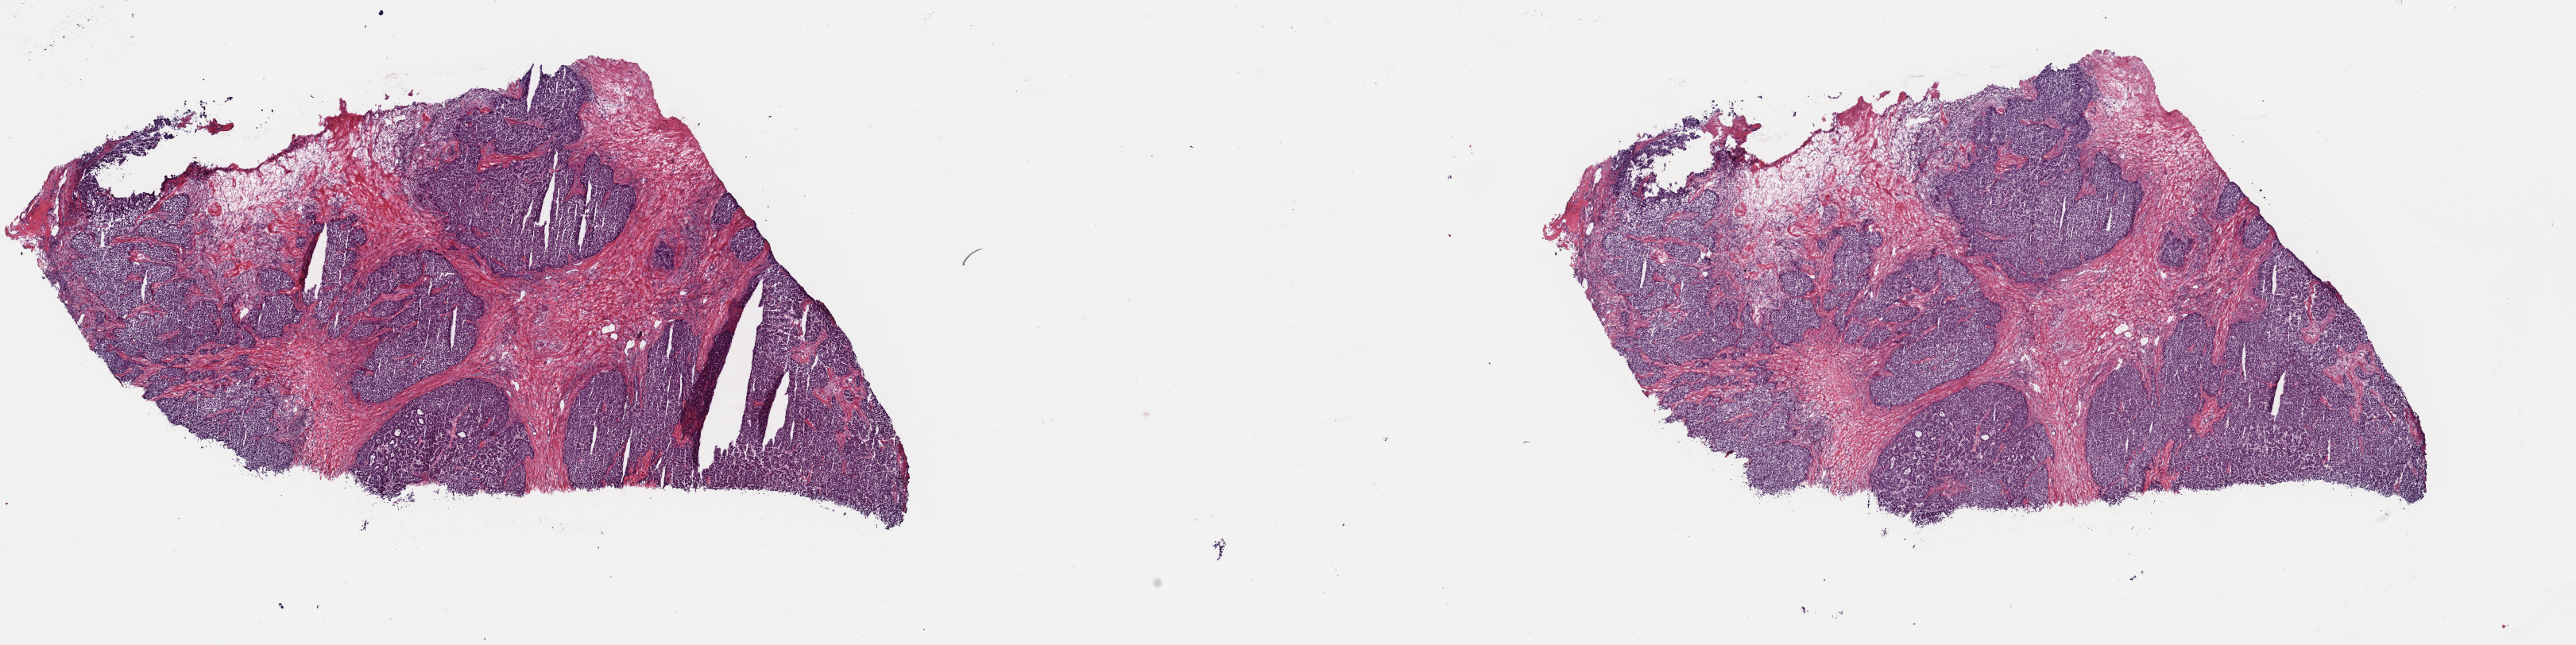
Whole-slide histology image, H&E, shown as a low-resolution overview of the whole scanned area (about 25.6 x 6.4 mm, acquisition: 40x scan), frozen section, liver, primary tumour sample. Patient: female, age at initial diagnosis 54 years. Histologic grade: G2 (moderately differentiated). Slide review estimates, as recorded: tumour cells 50%, tumour nuclei 100%, normal cells 0%, stromal cells 50%, necrosis 0%. Infiltration values recorded for this section: lymphocyte infiltration 4%, monocyte infiltration 1%, neutrophil infiltration 0%.
Diagnosis: Hepatocellular carcinoma, NOS. AJCC pathologic stage: II (7th edition).